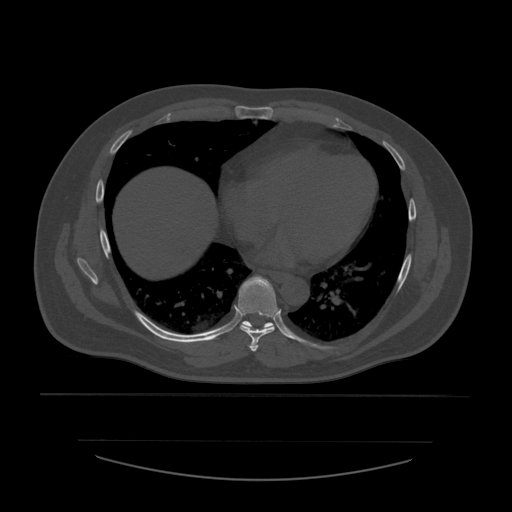
CT including the spine, one axial slice. Slice 352 of 532 in the series (ordered by position). 120 kVp. Bone window (W 1800 / L 400 HU). 1.25 mm slice thickness. 512 × 512 image matrix, field of view 441 × 441 mm. Patient age 44 years. From the clinical record (not read from this slice): primary cancer: soft tissue sarcoma.
Outlined on this slice (semi-automatically segmented with operator editing):
- T6 vertebra: bounding box (x1, y1, x2, y2) in pixels: (249, 341, 259, 353)
- T7 vertebra: (239, 276, 279, 343)
- T8 vertebra: (242, 321, 274, 331)